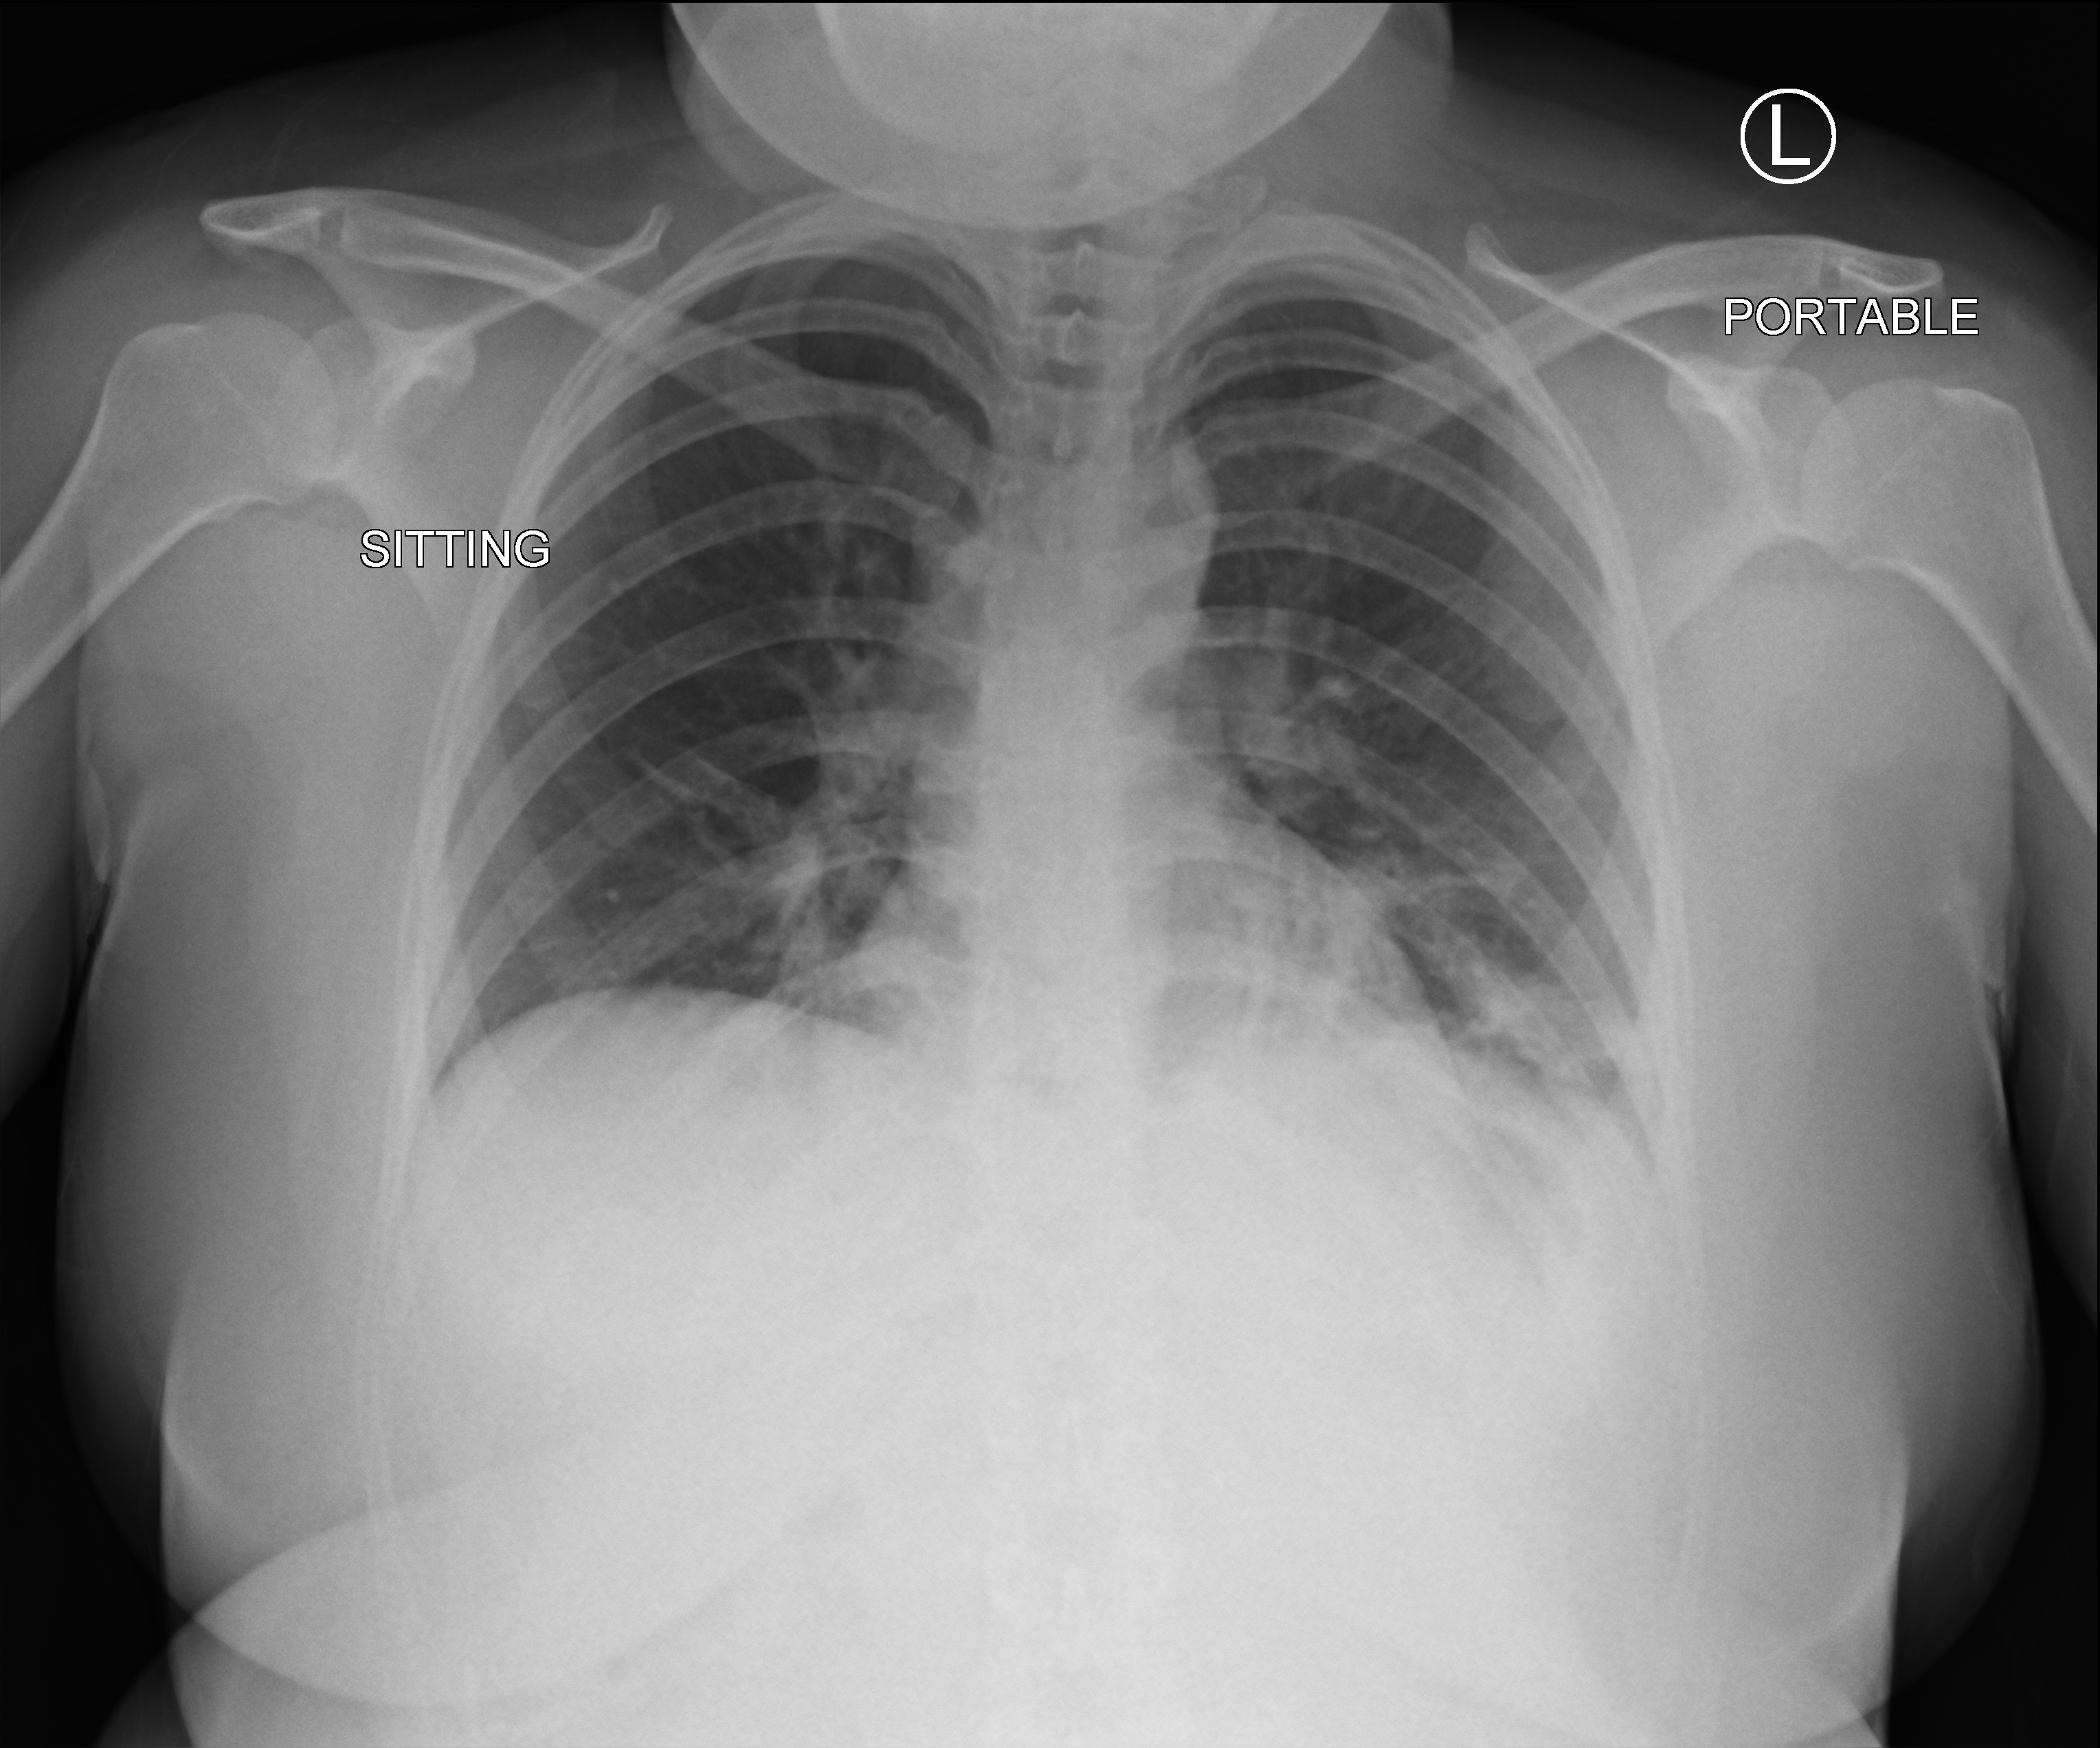
Portable chest radiograph; anteroposterior (AP) projection. Female patient hospitalised with COVID-19, age 18–59 years.
Hospital-stay facts (about this admission, not read from this image; timing relative to this image not recorded): admitted to intensive care during this hospital stay: no; smoking status (admission record): never; length of hospital stay: 1 day.